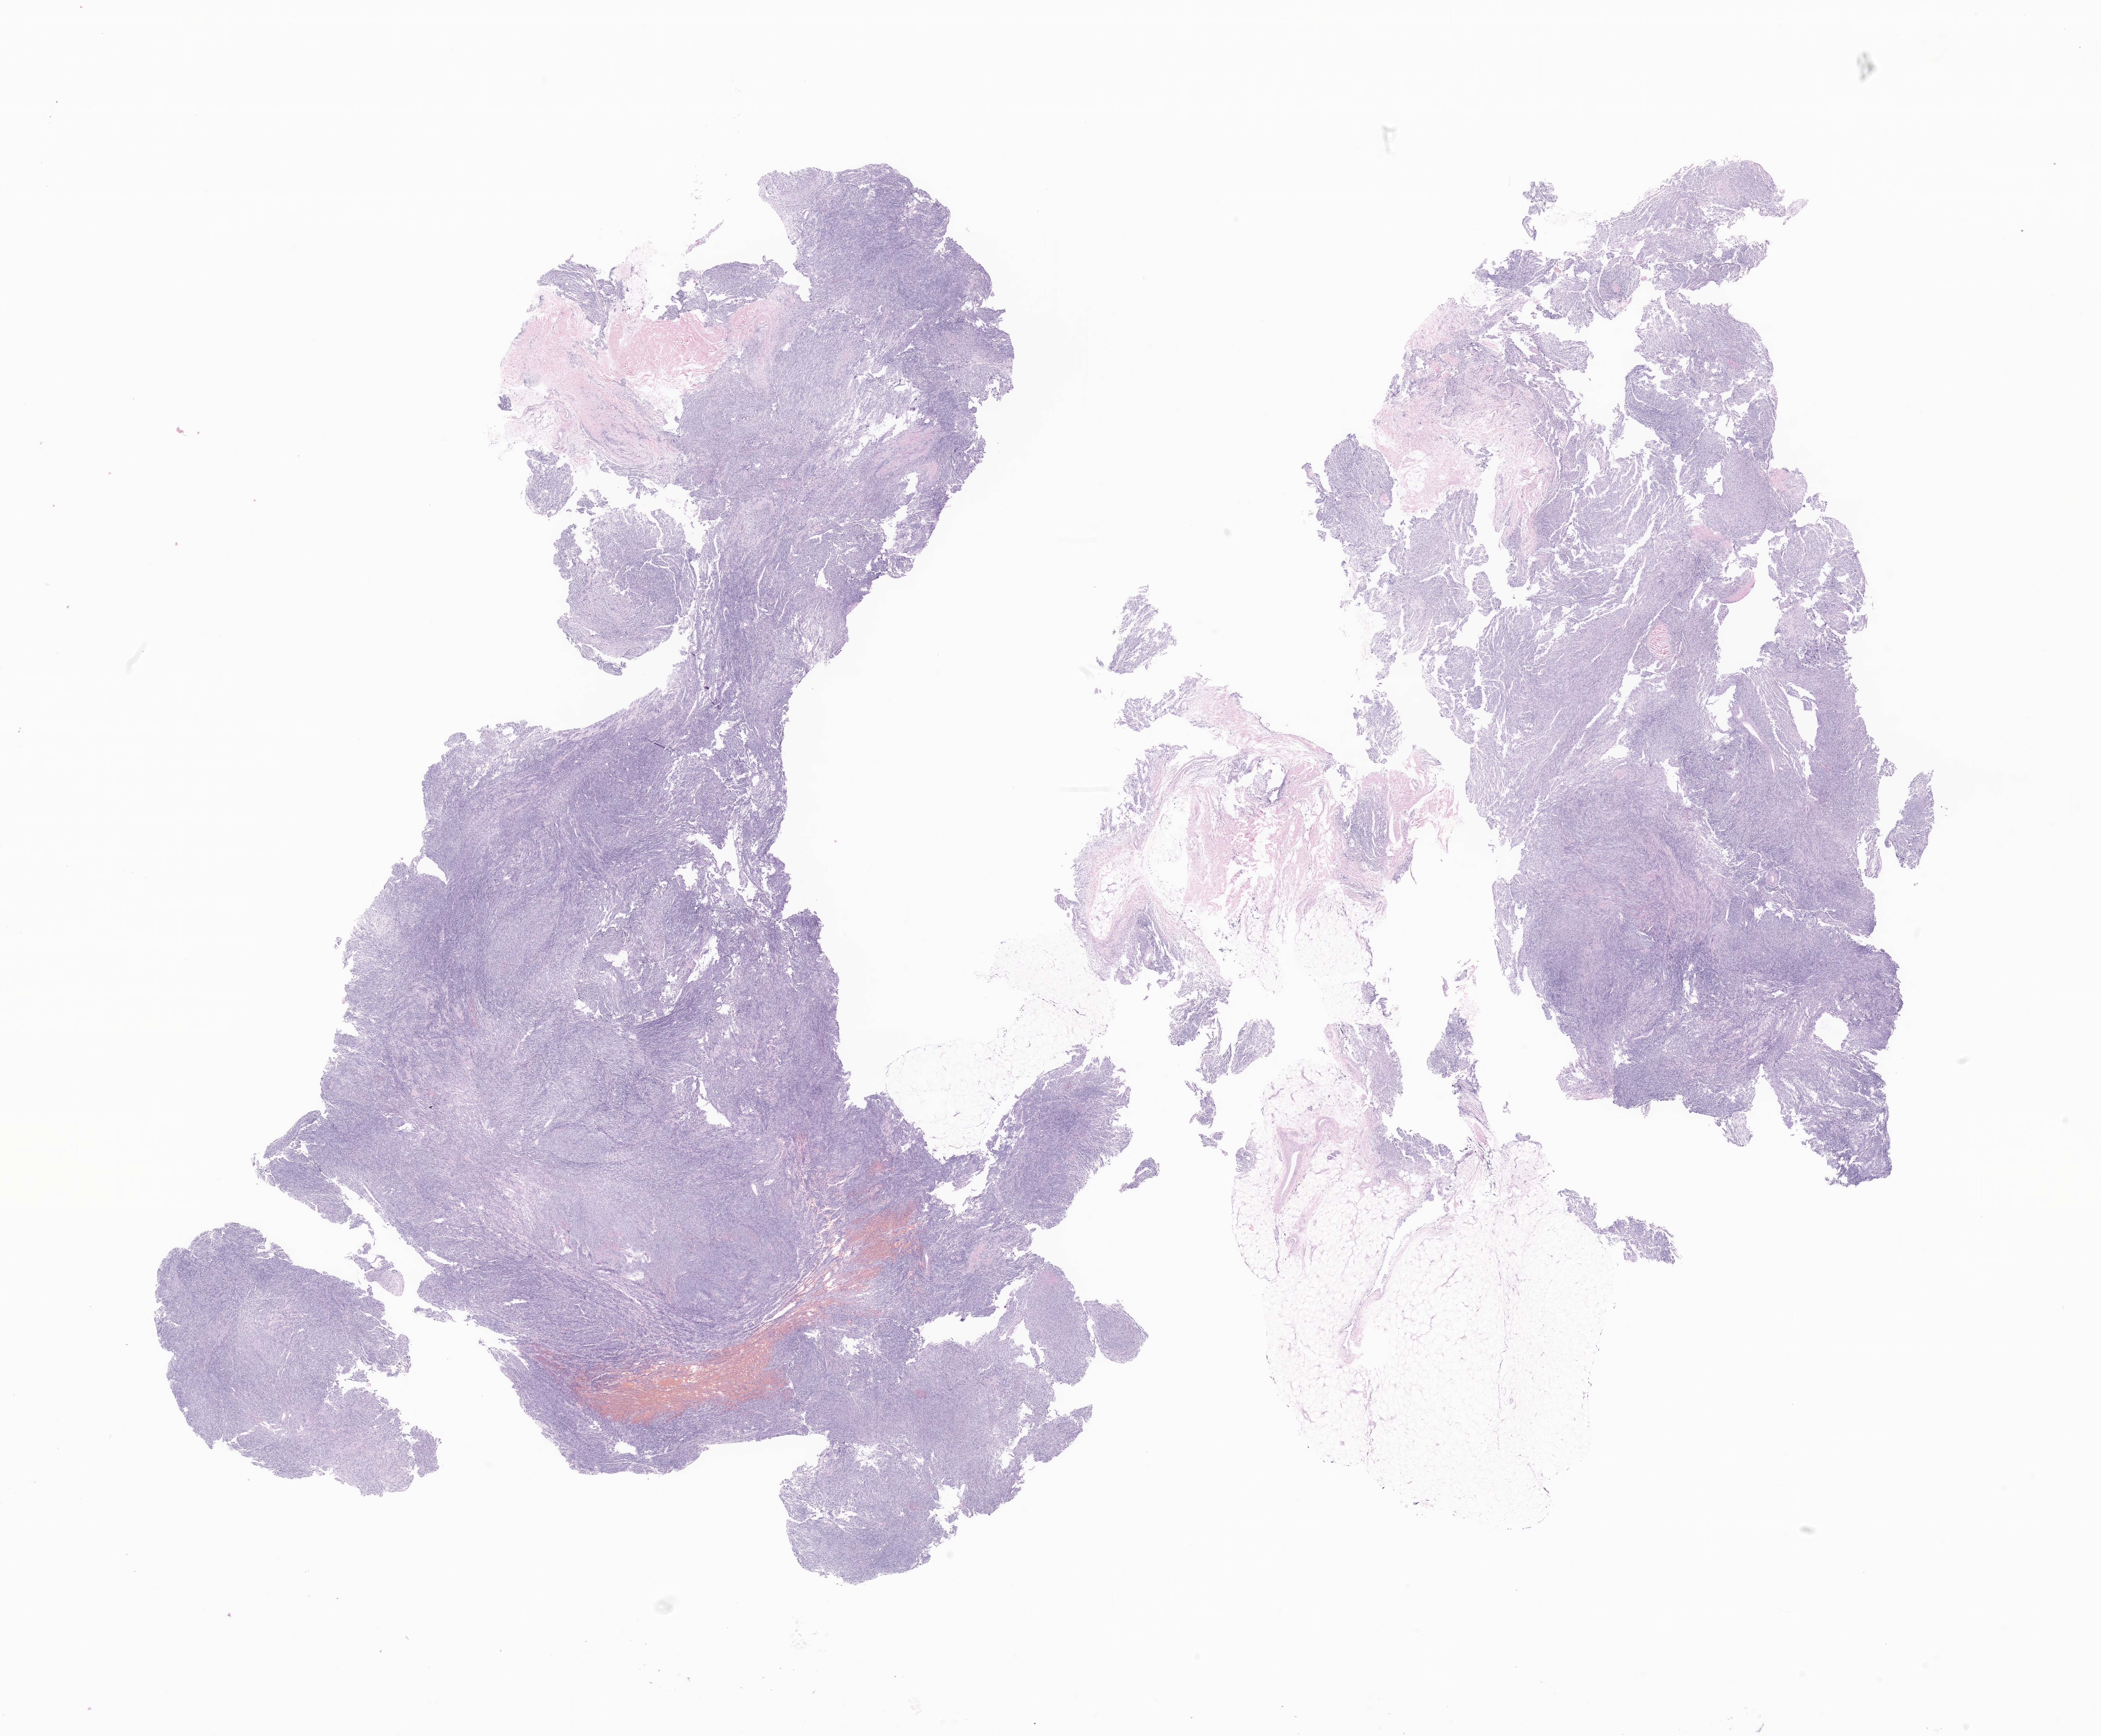
Digitized H&E-stained section of tumor tissue from the soft tissue of lower extremity — low-resolution overview of the scanned area, about 25.3 x 20.9 mm; FFPE section. Patient female; age 204 months (17 years).
Recorded diagnosis: Synovial sarcoma, NOS.